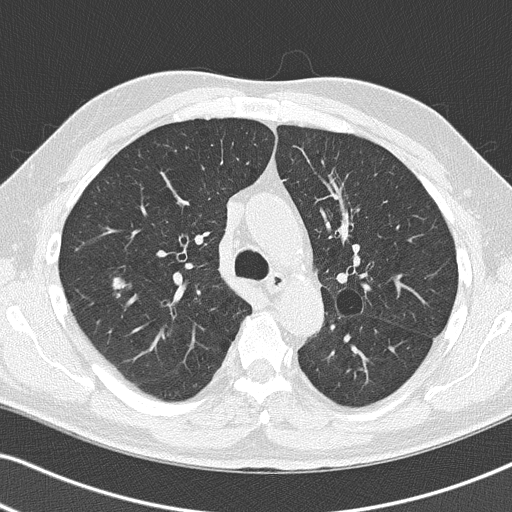
Low-dose screening chest CT, one axial slice. Slice 90 of 140 in the series (ordered by position). Reconstruction kernel B50f. 120 kVp. Lung window (W 1500 / L -600 HU). 2 mm slice thickness. 512 × 512 image matrix, field of view 330 × 330 mm.
Structures marked on this image (expert manual segmentation):
- lesion 1 (tumor, upper lobe of right lung): bounding box <112,277,126,289> (left, top, right, bottom; pixels)